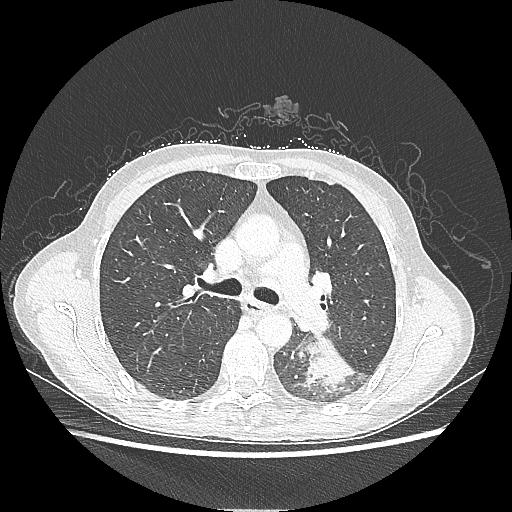
Chest CT, one axial slice; position 138 of 220 along the scan axis; 80 kVp; lung window (W 1500 / L -600 HU); 1.25 mm slice thickness; 512 × 512 image matrix, field of view 360 × 360 mm. Female patient, age 53 years. Case-level facts recorded for this patient, not image findings: clinical TNM (as recorded): T3 N0 M0.
Structures marked on this image (bounding box drawn by a radiologist):
- lung tumour (recorded histology: adenocarcinoma): box from (x=301, y=336) to (x=358, y=394) px